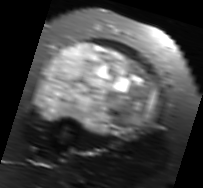
MRI of an extremity soft-tissue mass, one axial slice. Position 40 of 91 along the scan axis. T2-weighted fat-saturated. MR volume resampled by the dataset authors to the PET/CT grid (not the native acquisition matrix). 203 × 188 image matrix, field of view 198 × 184 mm. Female patient. From the clinical record (not read from this slice): histological type: malignant solitary fibrous tumor; grade: intermediate; site of the primary tumour: right thigh.
Annotated regions visible in this slice (expert contour drawn on MRI and transferred to this co-registered scan by the dataset authors):
- gross tumour volume including surrounding oedema: bounding box (x1, y1, x2, y2) in pixels: (33, 42, 162, 139)
- gross tumour volume (mass): (40, 42, 157, 136)